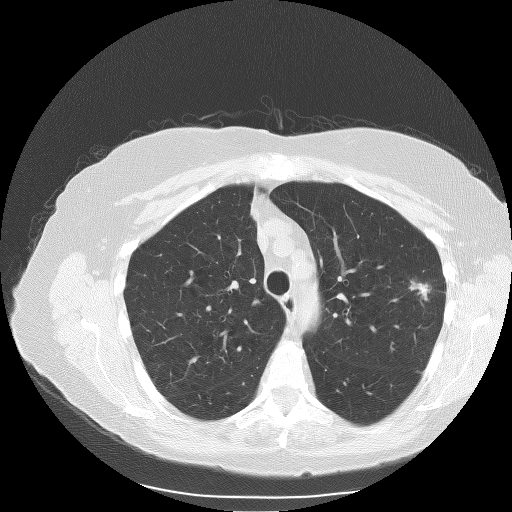
Axial slice from a low-dose chest CT screening exam. Baseline screening round. Lung window (W 1500 / L -600 HU). 2.5 mm slice thickness. Lung (sharp) reconstruction kernel (BONE). 512 × 512 image matrix. Female, age 71 years at enrolment. Former smoker at enrolment.
Lesion marked by an expert reader, bounding box <403,277,442,312> (left, top, right, bottom; pixels). The exam's reader record, not a measurement of the box and not confirmed to be the same lesion: non-calcified nodule or mass ≥4 mm, left upper lobe, 15 × 9 mm, spiculated (stellate) margins, soft tissue attenuation. Official screen result: positive, change unspecified: nodule(s) >= 4 mm or enlarging nodule(s), mass(es), or other non-specific abnormalities suspicious for lung cancer.